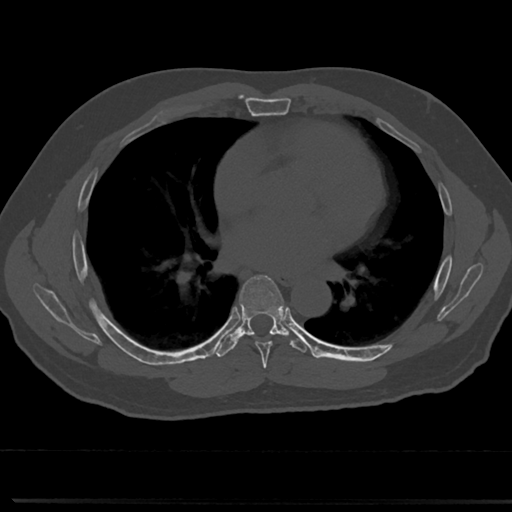
CT including the spine, one axial slice; position 424 of 817 along the scan axis; bone window (W 1800 / L 400 HU); 0.5 mm slice thickness; 512 × 512 image matrix, field of view 355 × 355 mm. Patient: male, 61 years. From the clinical record (not read from this slice): primary cancer: prostate.
Annotated regions visible in this slice (semi-automatically segmented with operator editing):
- T6 vertebra: bounding box (x1, y1, x2, y2) in pixels: (239, 275, 288, 359)
- T7 vertebra: (239, 324, 285, 335)